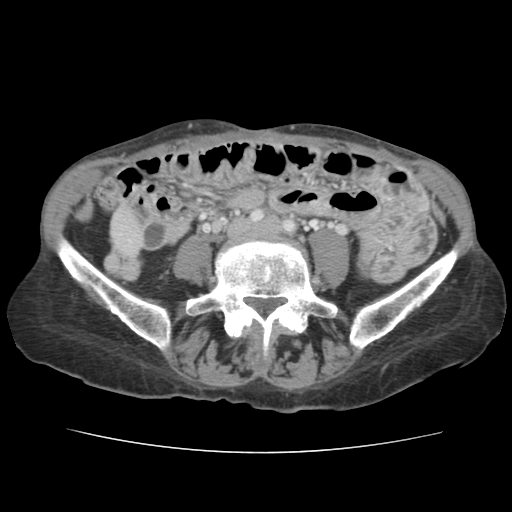
Contrast-enhanced abdominal CT, one axial slice; position 9 of 136 along the scan axis; 120 kVp; soft-tissue window (W 400 / L 40 HU); 2.5 mm slice thickness; 512 × 512 image matrix, field of view 319 × 319 mm. Female patient, age 77 years. From the clinical record (not read from this slice): diagnosis: colorectal cancer liver metastases, imaged before liver resection; multiple liver metastases: yes; largest metastasis: 3 cm; chemotherapy before resection: yes.
Structures marked on this image (manually delineated by an expert):
- liver: box from (x=113, y=210) to (x=142, y=253) px